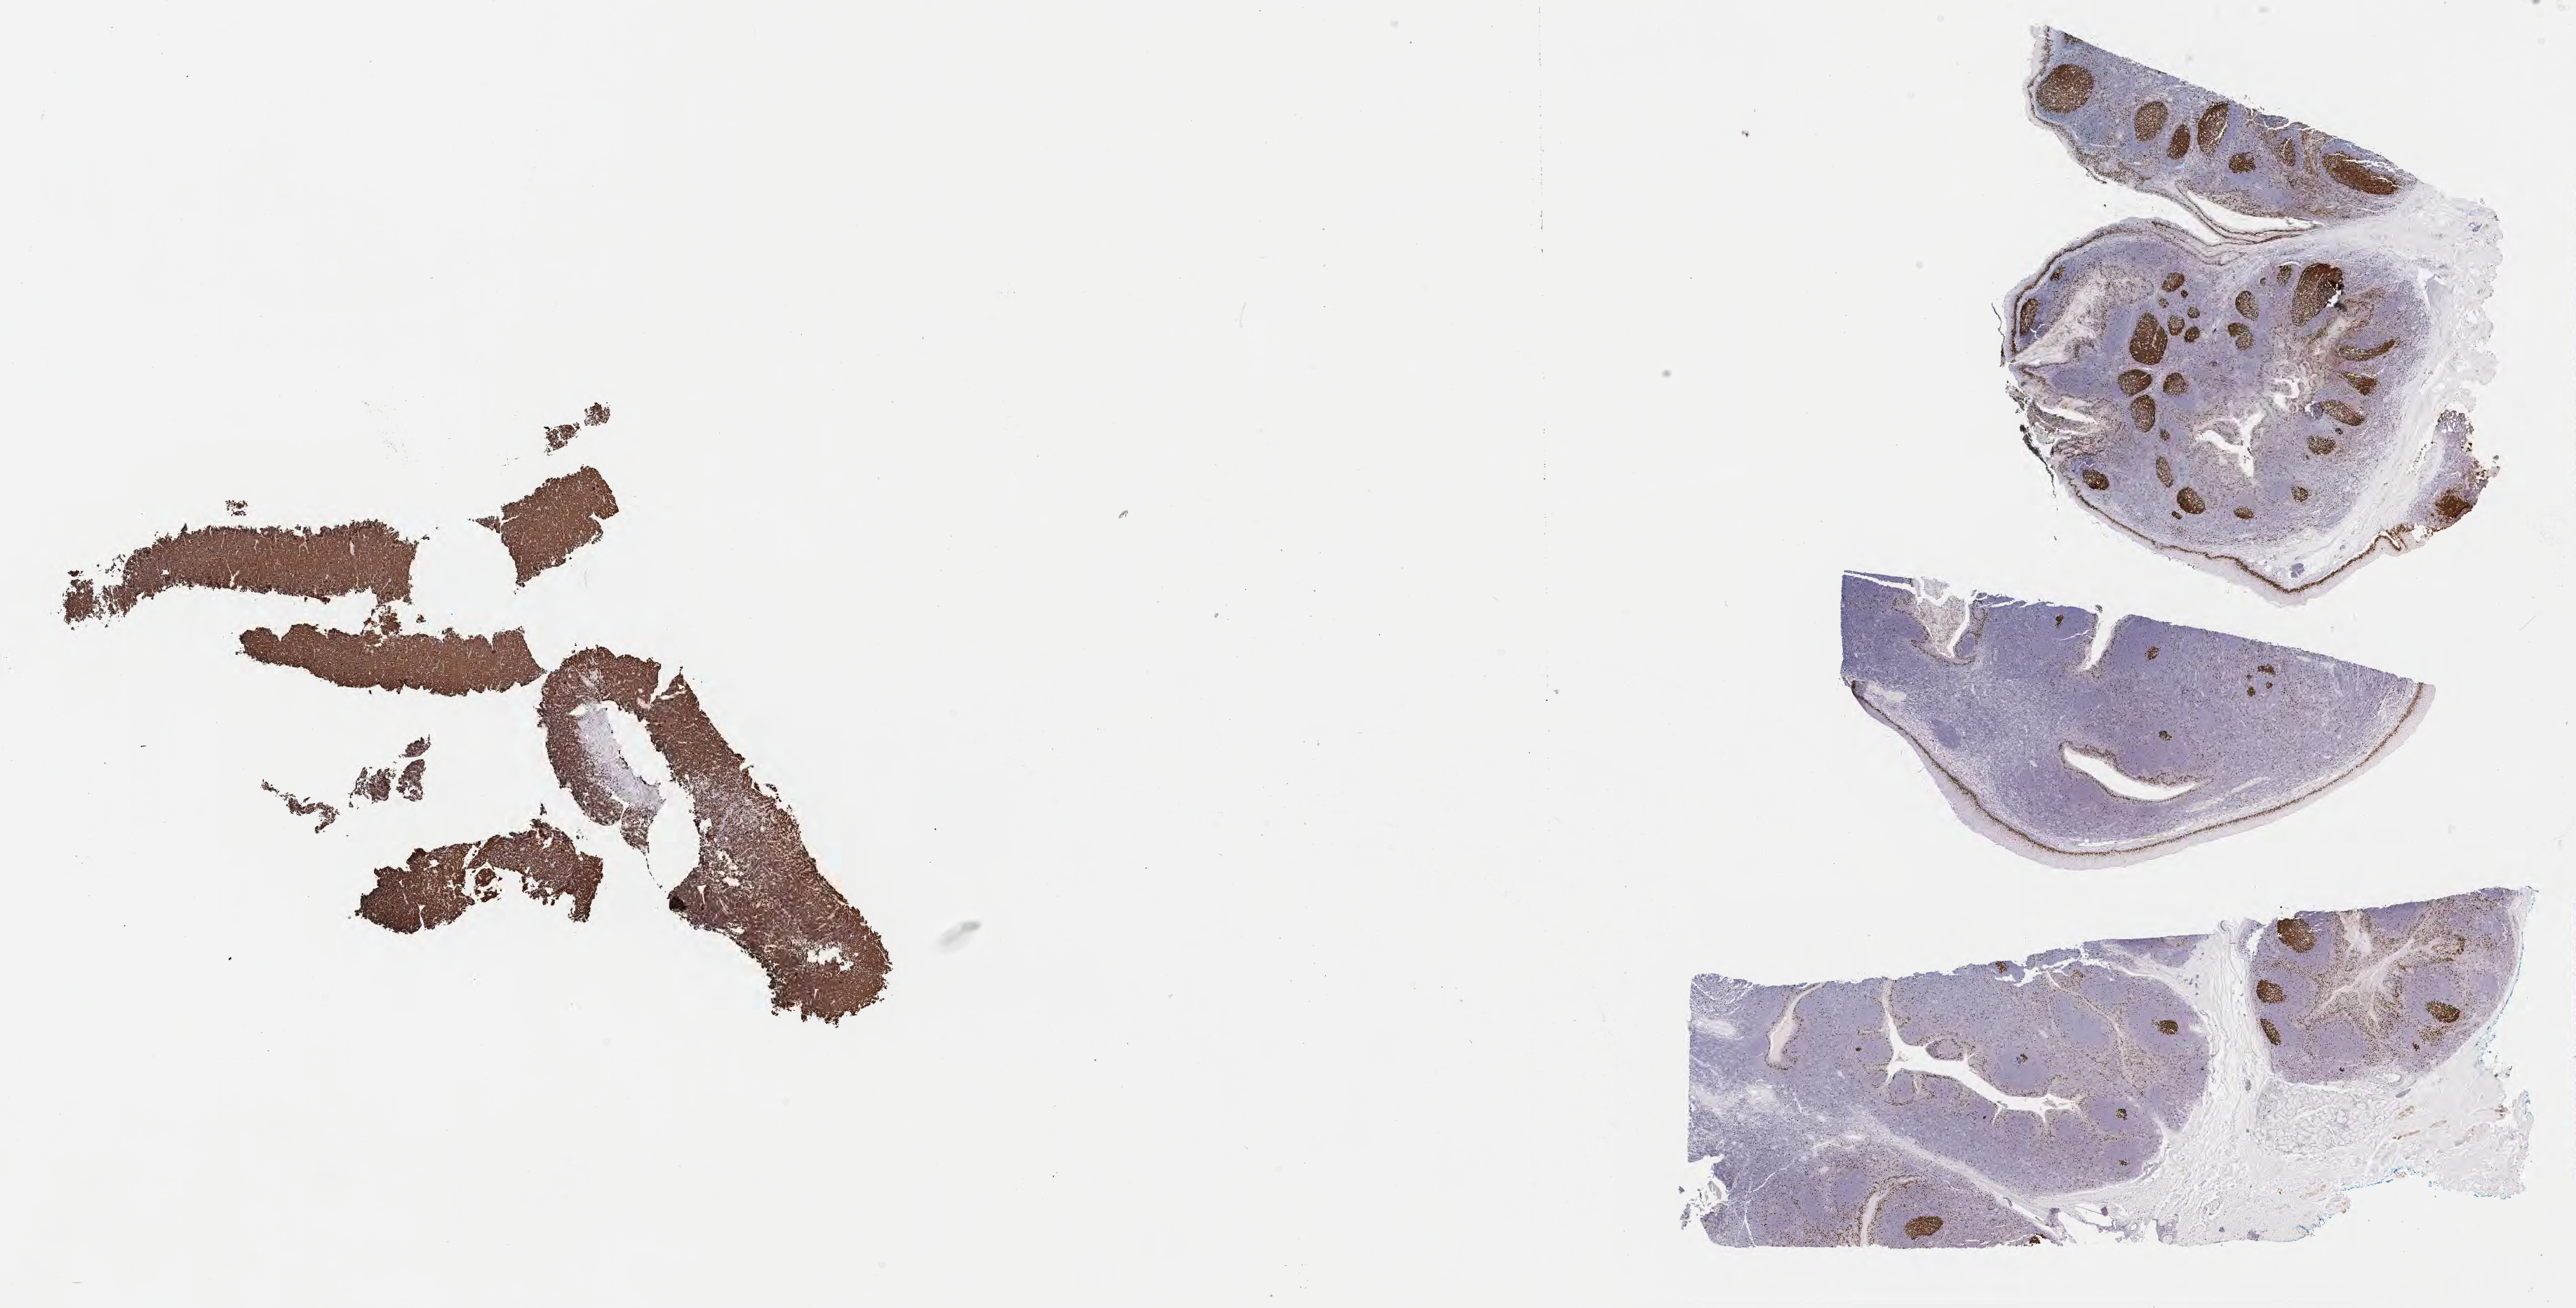
IHC for Ki-67, whole-slide image, a low-resolution overview of the entire scanned area, about 29.7 x 15.1 mm; specimen: tumor tissue; site: liver. Male, age 4 years at initial diagnosis.
Histologic diagnosis: Burkitt lymphoma, NOS.